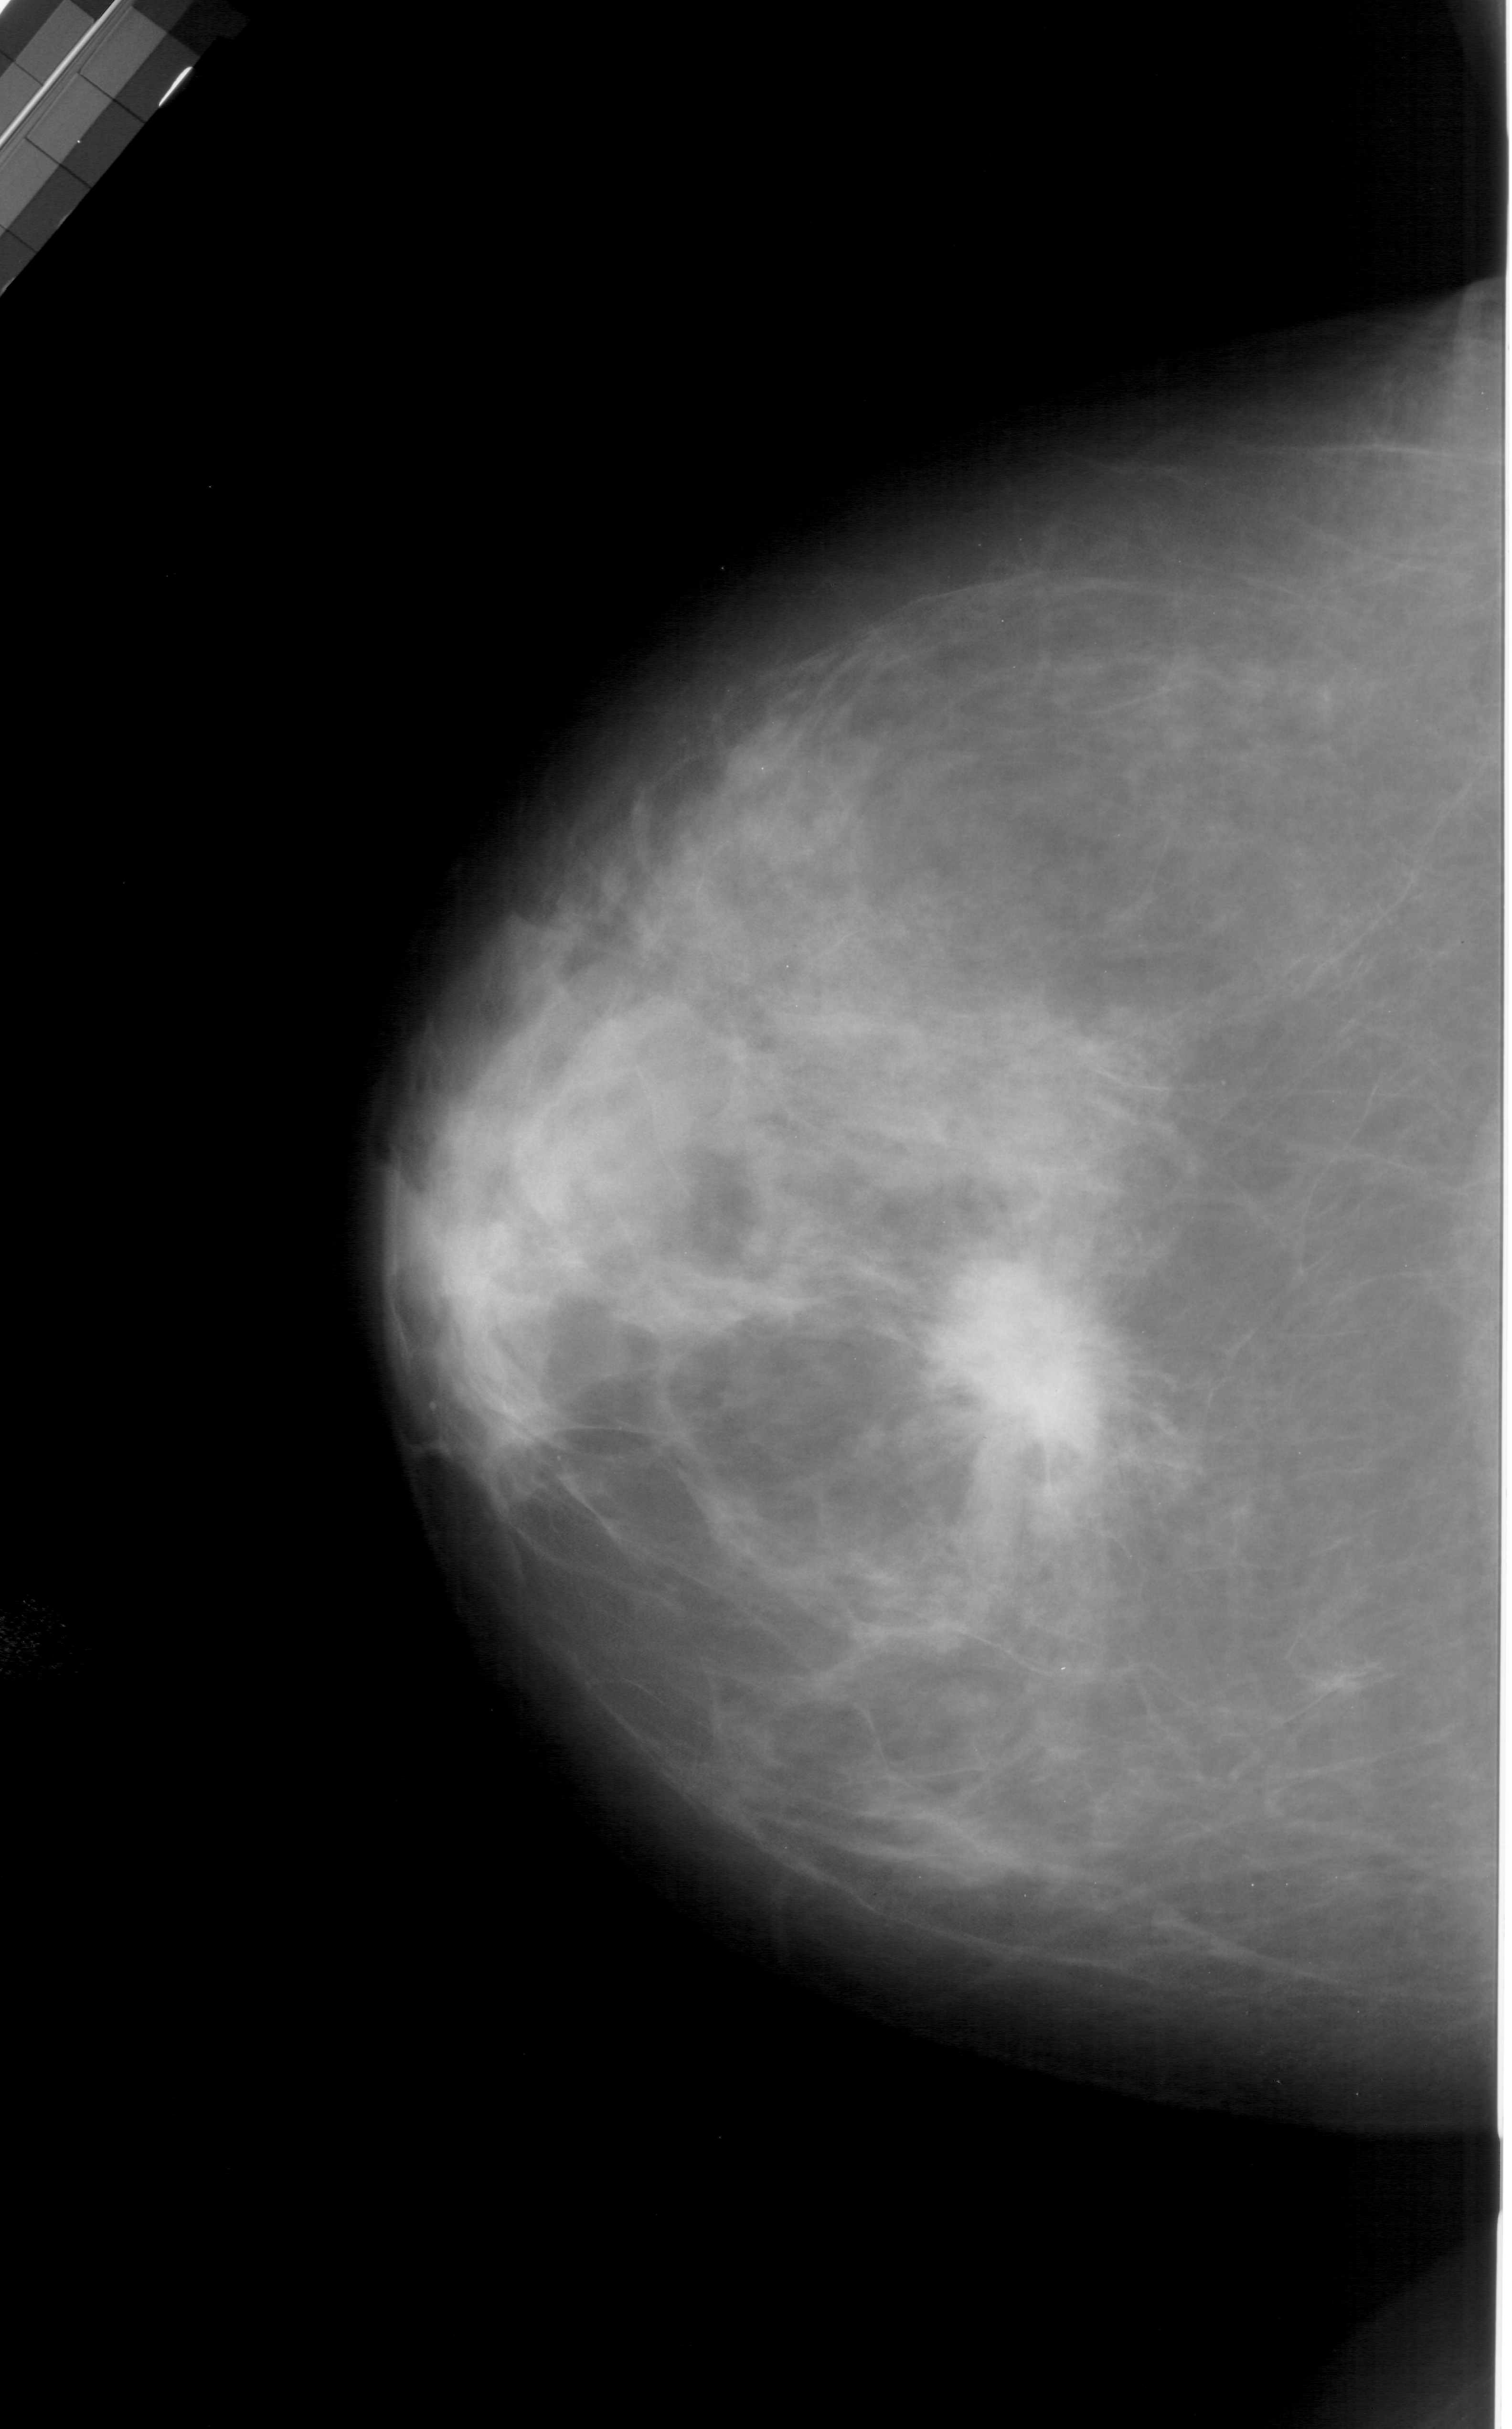
Digitized screen-film mammogram. Left breast. CC view. BI-RADS breast density category 3 (scale 1–4). 1512 × 2429 image matrix.
Expert-marked regions of interest on this film, with their recorded descriptors:
- mass, shape irregular, margins spiculated; BI-RADS assessment category 5; subtlety rating 5 on a 1 (subtle) to 5 (obvious) scale; pathology (as recorded): malignant: bounding box (x1, y1, x2, y2) in pixels: (911, 1286, 1102, 1481)